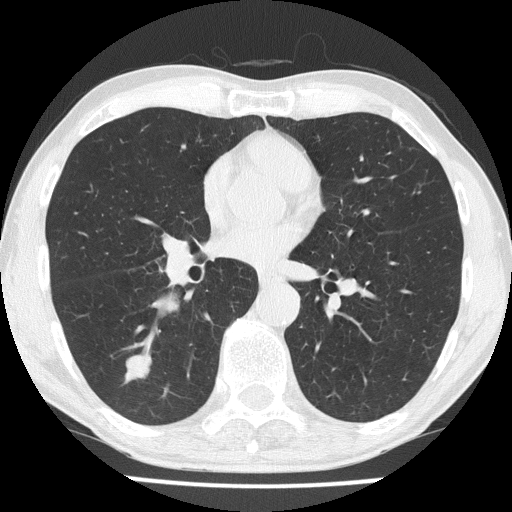
Low-dose screening chest CT, one axial slice. Slice 83 of 186 in the series (ordered by position). 120 kVp. Lung window (W 1500 / L -600 HU). 2 mm slice thickness. 512 × 512 image matrix, field of view 328 × 328 mm.
Structures marked on this image (expert manual segmentation):
- lesion 1 (tumor, lower lobe of right lung): bounding box <124,353,152,384> (left, top, right, bottom; pixels)